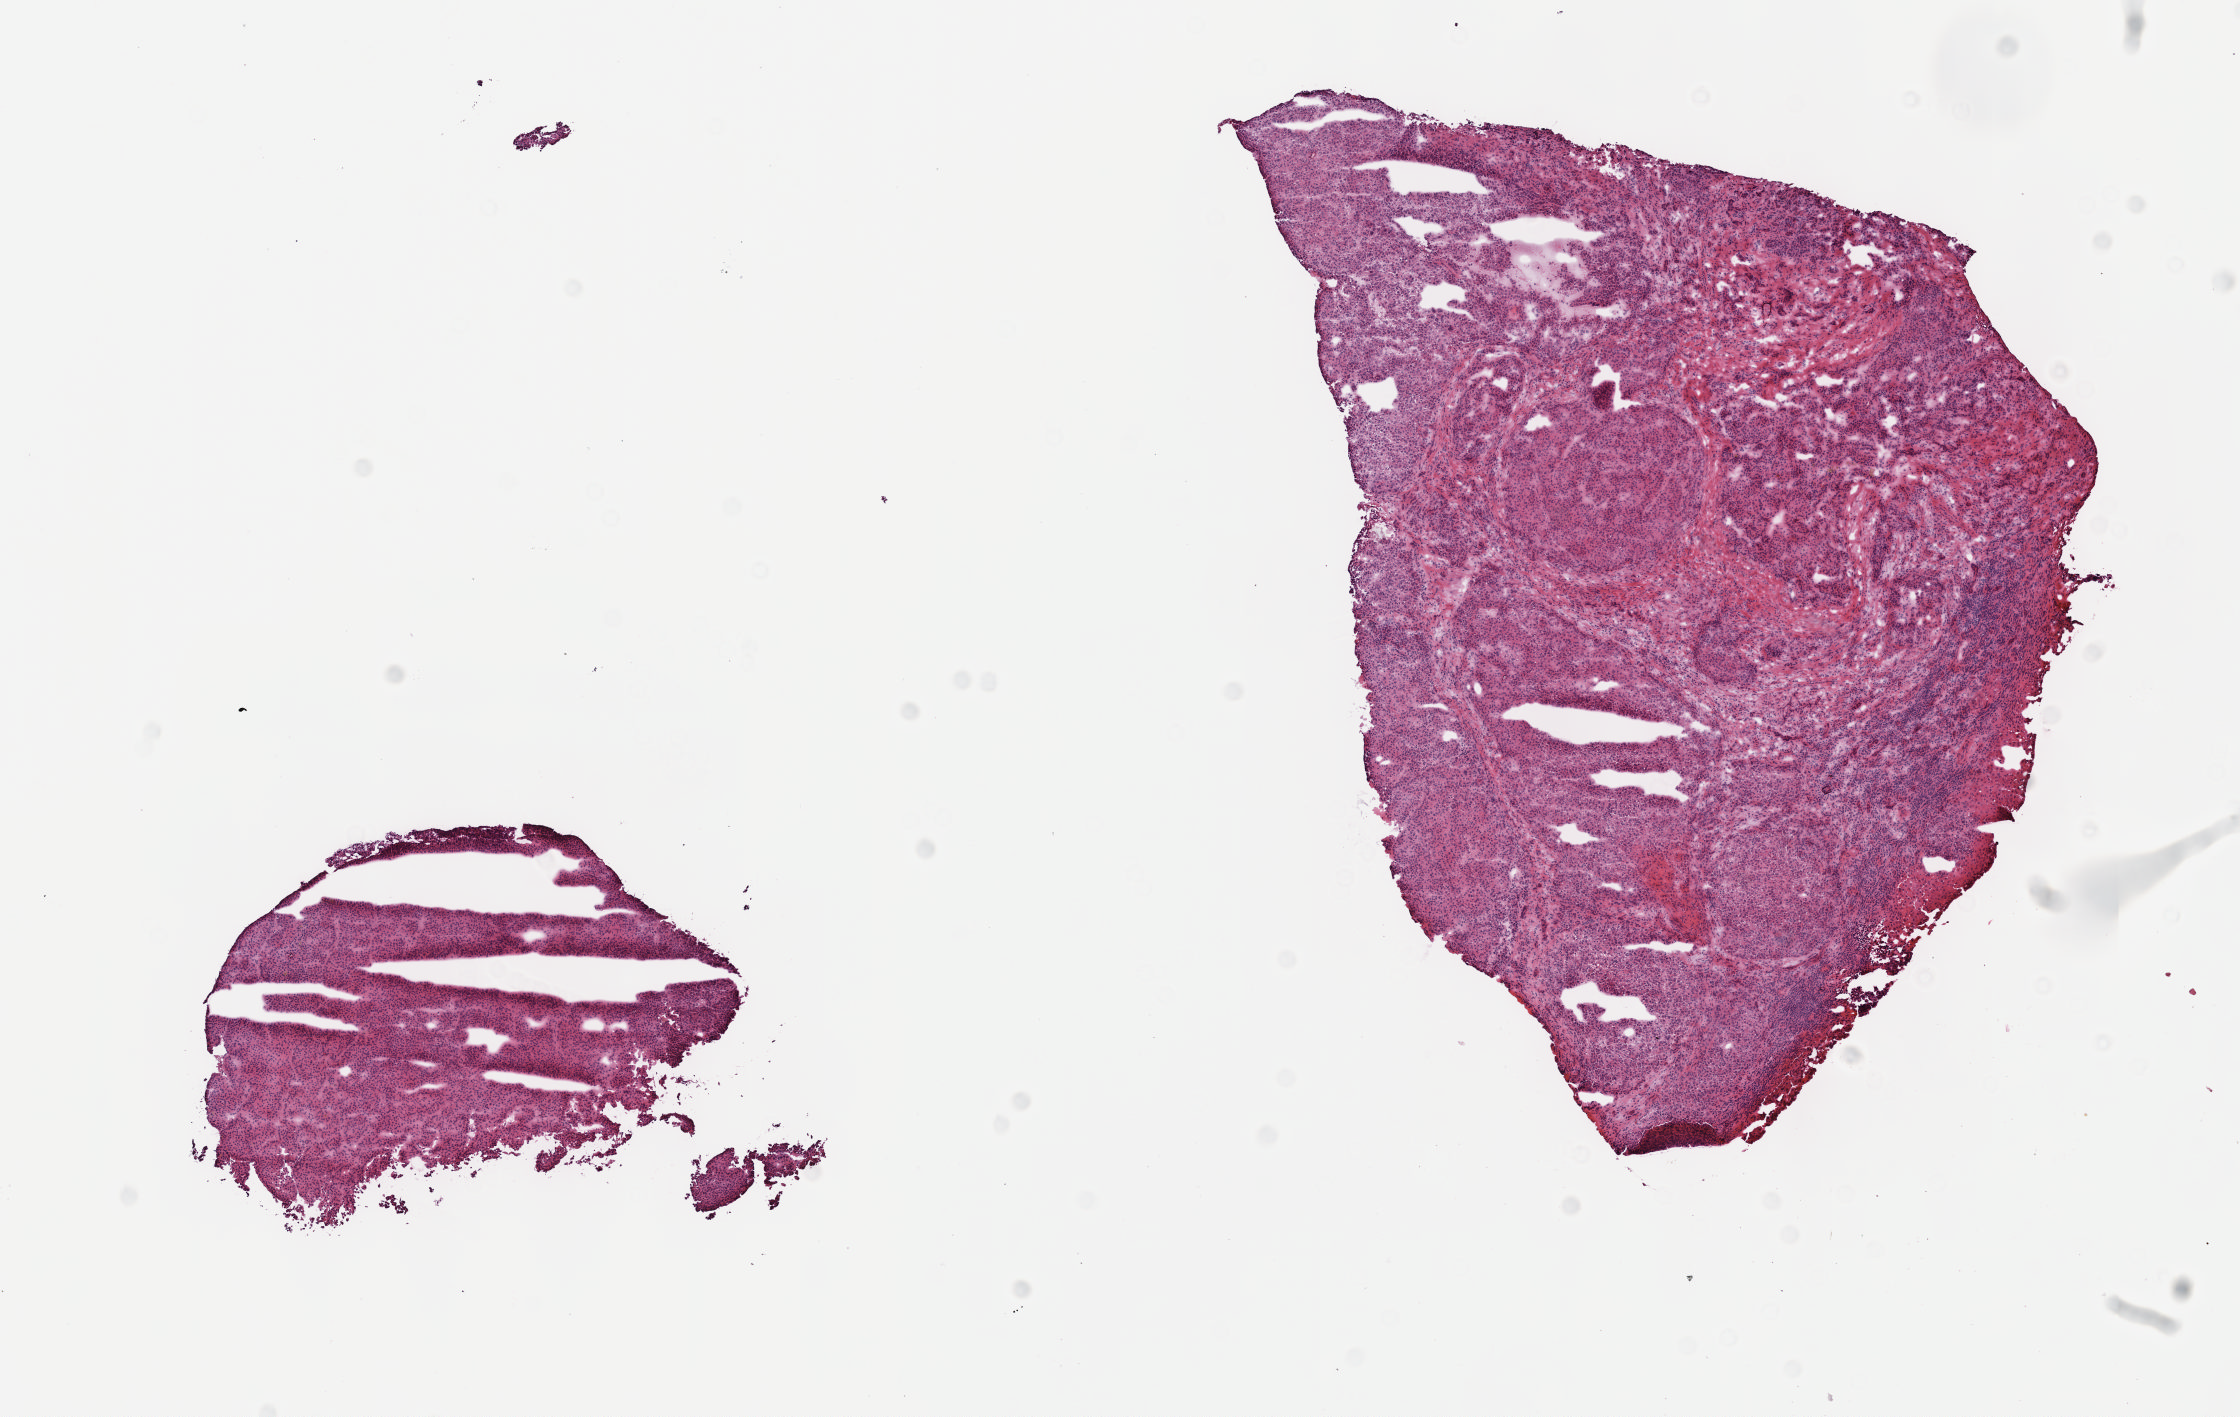
Whole-slide histology image, H&E — shown as a low-resolution overview of the whole scanned area (about 9.1 x 5.7 mm, slide scanned at 40x). Frozen section. Sample: primary tumour, liver. Male patient; age at initial diagnosis 45 years. Histologic grade: G3 (poorly differentiated). Pathologist review of this section (percent, as recorded): tumour cells 100%, tumour nuclei 70%, normal cells 0%, stromal cells 0%, necrosis 0%. Inflammatory infiltration, as recorded: lymphocyte infiltration 3%, monocyte infiltration 0%, neutrophil infiltration 0%.
Histologic diagnosis: Hepatocellular carcinoma, NOS. AJCC pathologic stage: I. TNM: T1 N0 M0.